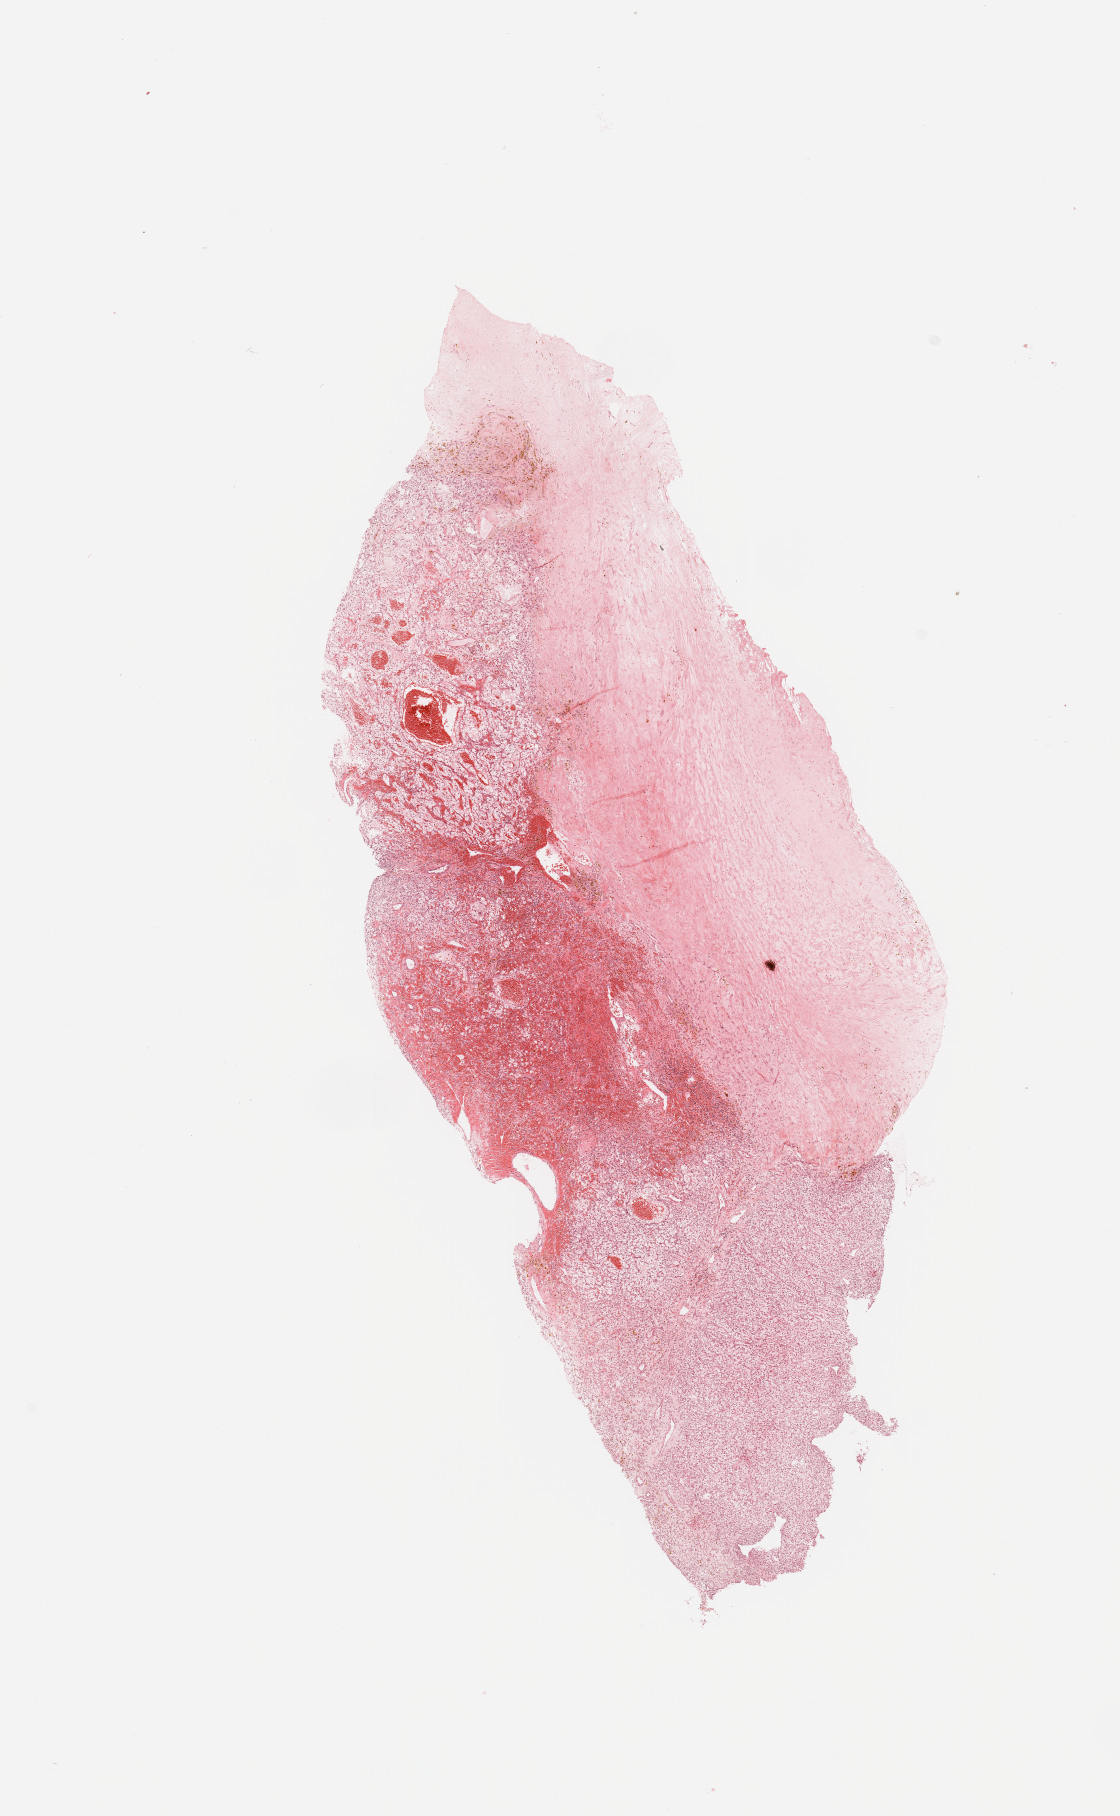
Digitized Hematoxylin and eosin (H&E) stained tissue section (whole slide), a low-resolution overview of the entire scanned area, about 8.9 x 14.4 mm. Tumour tissue sample, sampled site: kidney. Patient: male, age 44 years. Histologic grade: G2 (moderately differentiated). Slide review estimates, as recorded: tumour nuclei 80%, necrosis 5%.
Diagnosis: Renal cell carcinoma, NOS. Primary tumour site (as recorded): middle. AJCC pathologic stage: I.